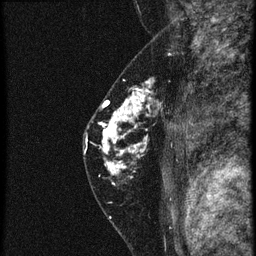
Breast MRI (dynamic contrast-enhanced), one sagittal slice; 4 images stored at this slice position (order not interpretable as contrast timing); 1.5 T; TE 4.2 ms, TR 20.4 ms; 256 × 256 image matrix. Patient: female, 46 years. From the clinical record (not read from this slice): setting: breast cancer imaged before/during neoadjuvant chemotherapy; receptor status: triple-negative.
Structures marked on this image (semi-automatically segmented with operator editing):
- analysis volume of interest (the breast-tissue region the enhancement analysis was run in; not a lesion): bounding box <88,82,181,185> (left, top, right, bottom; pixels)
- tumour enhancement mask (voxels above the 90 % enhancement threshold inside the analysis volume of interest): <102,82,155,185>